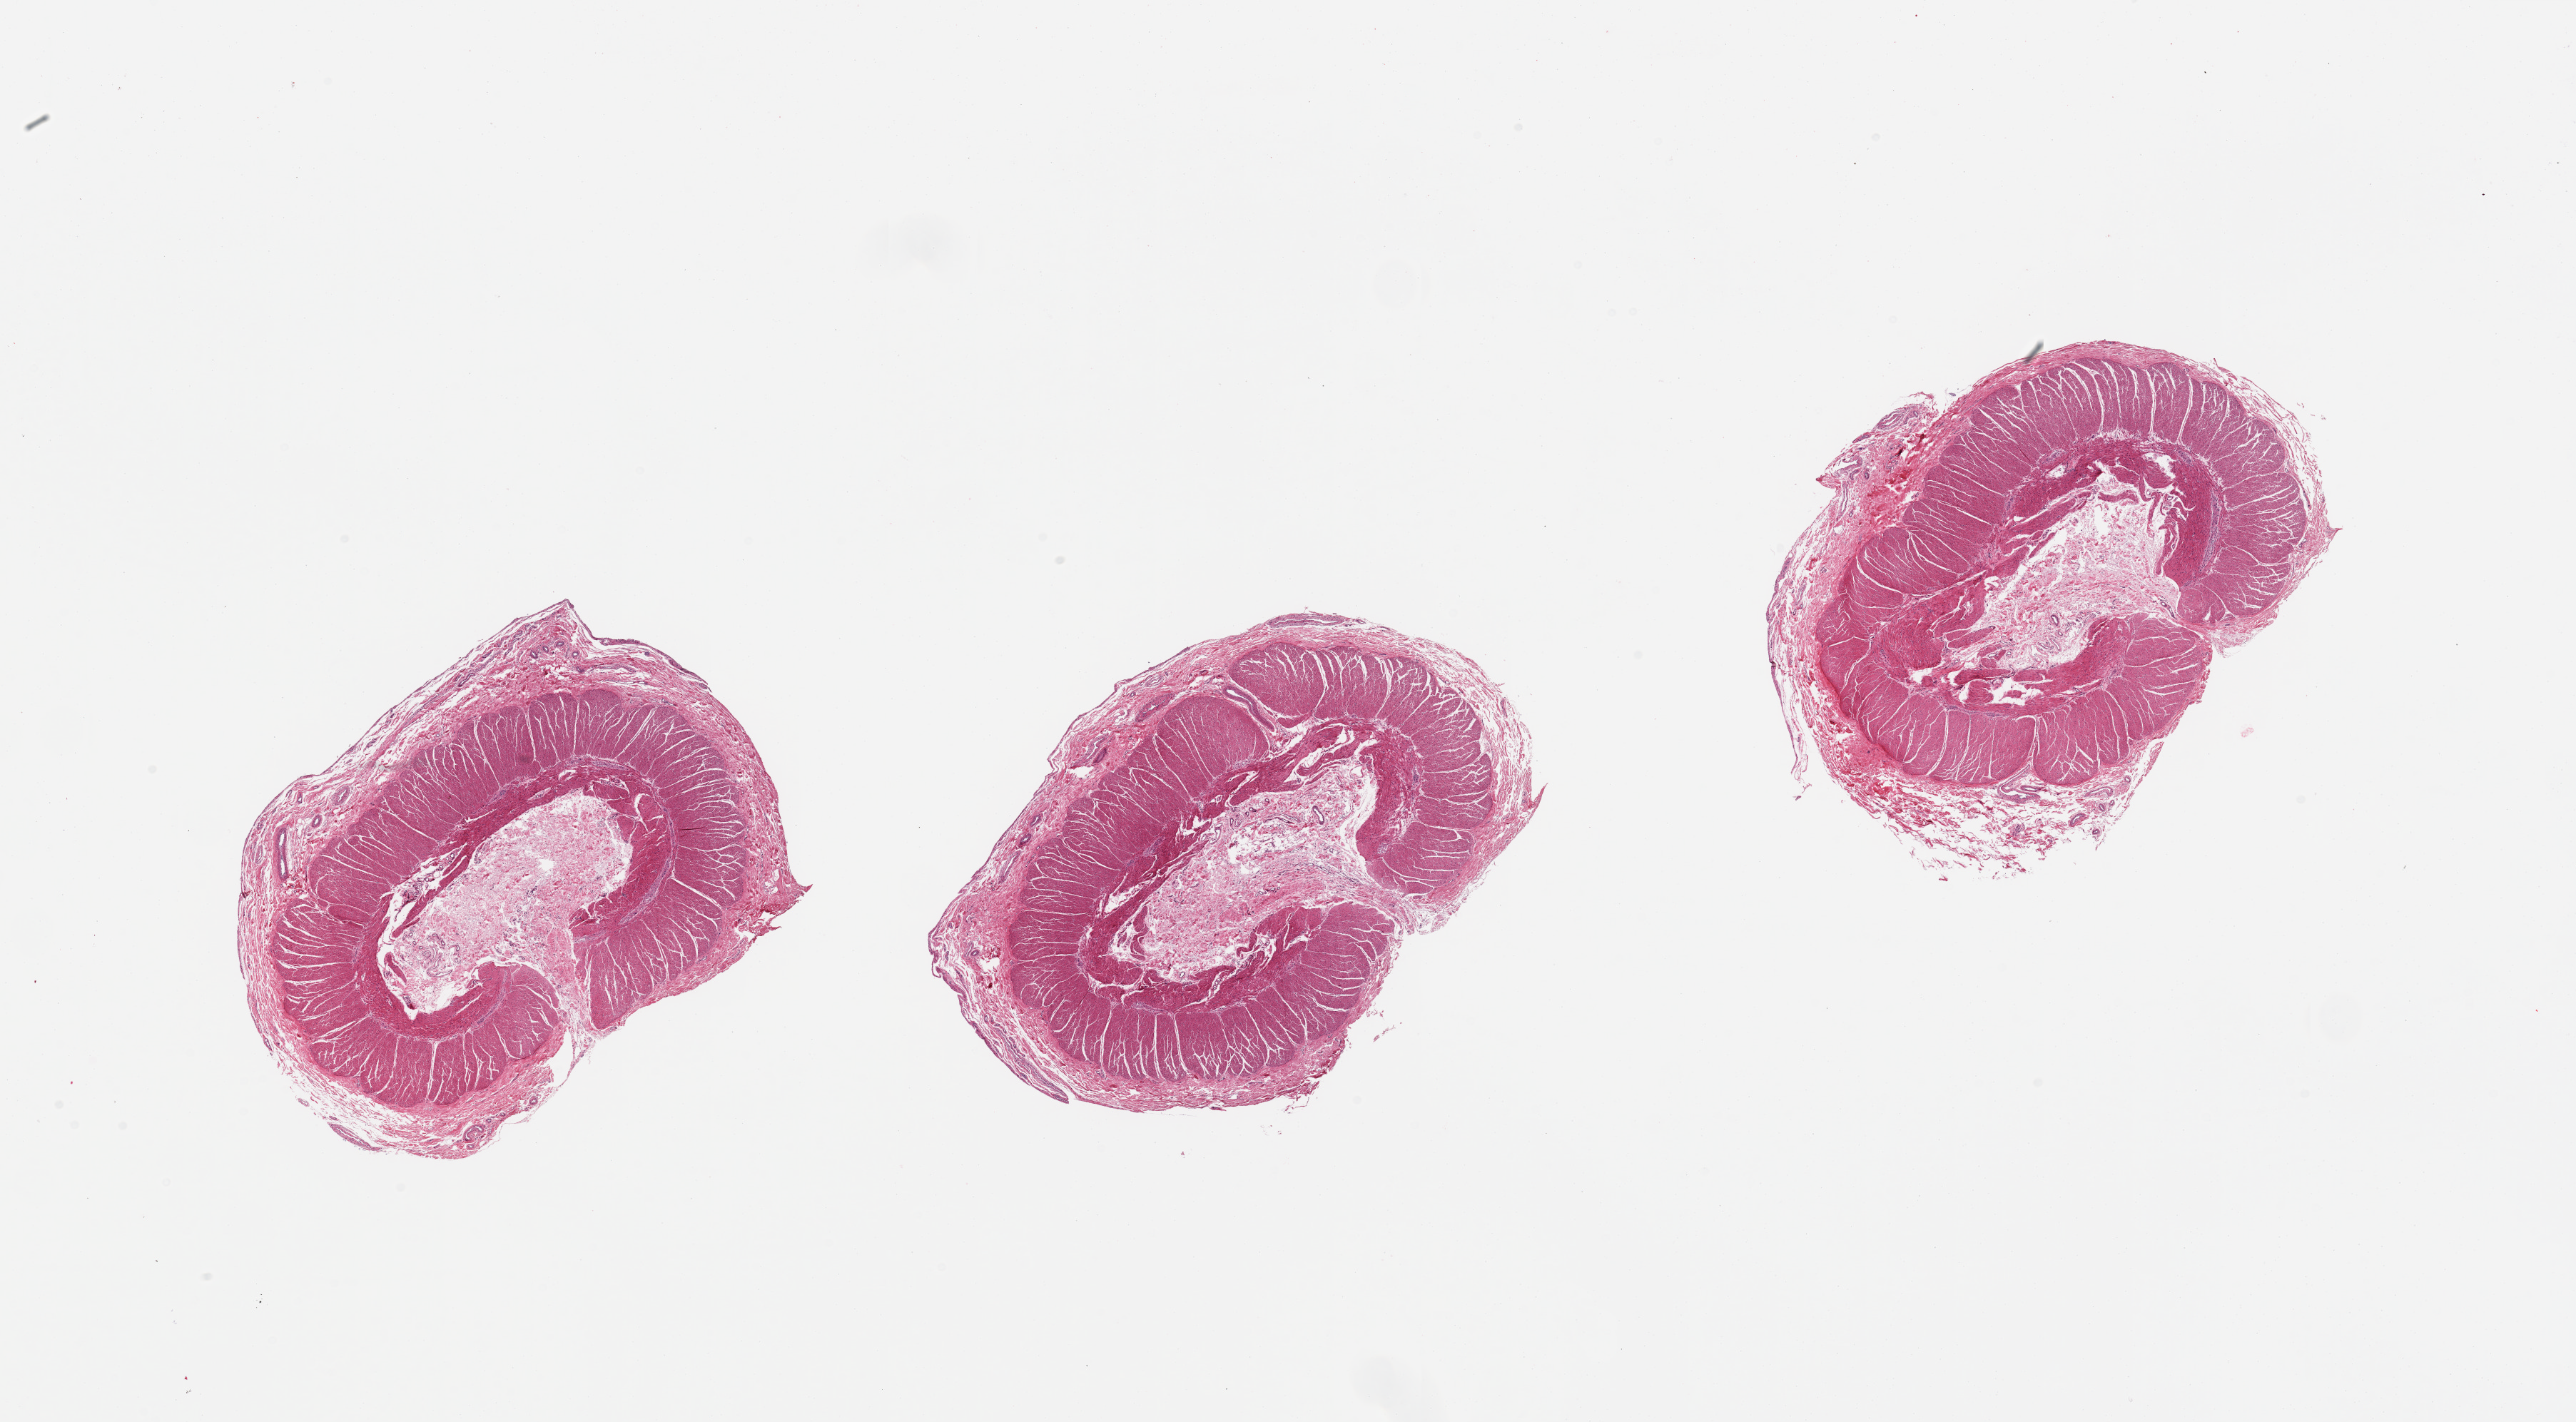
Haematoxylin and eosin whole-slide image, brightfield, whole scanned area (about 28.5 x 15.8 mm) shown as a low-resolution overview; PAXgene-fixed, paraffin-embedded tissue; sampled site (target tissue): transverse colon; donor tissue sample. Donor sex: male.
• reviewer comment on this tissue sample: 3 pieces; muscularis only, no mucosa (also target)